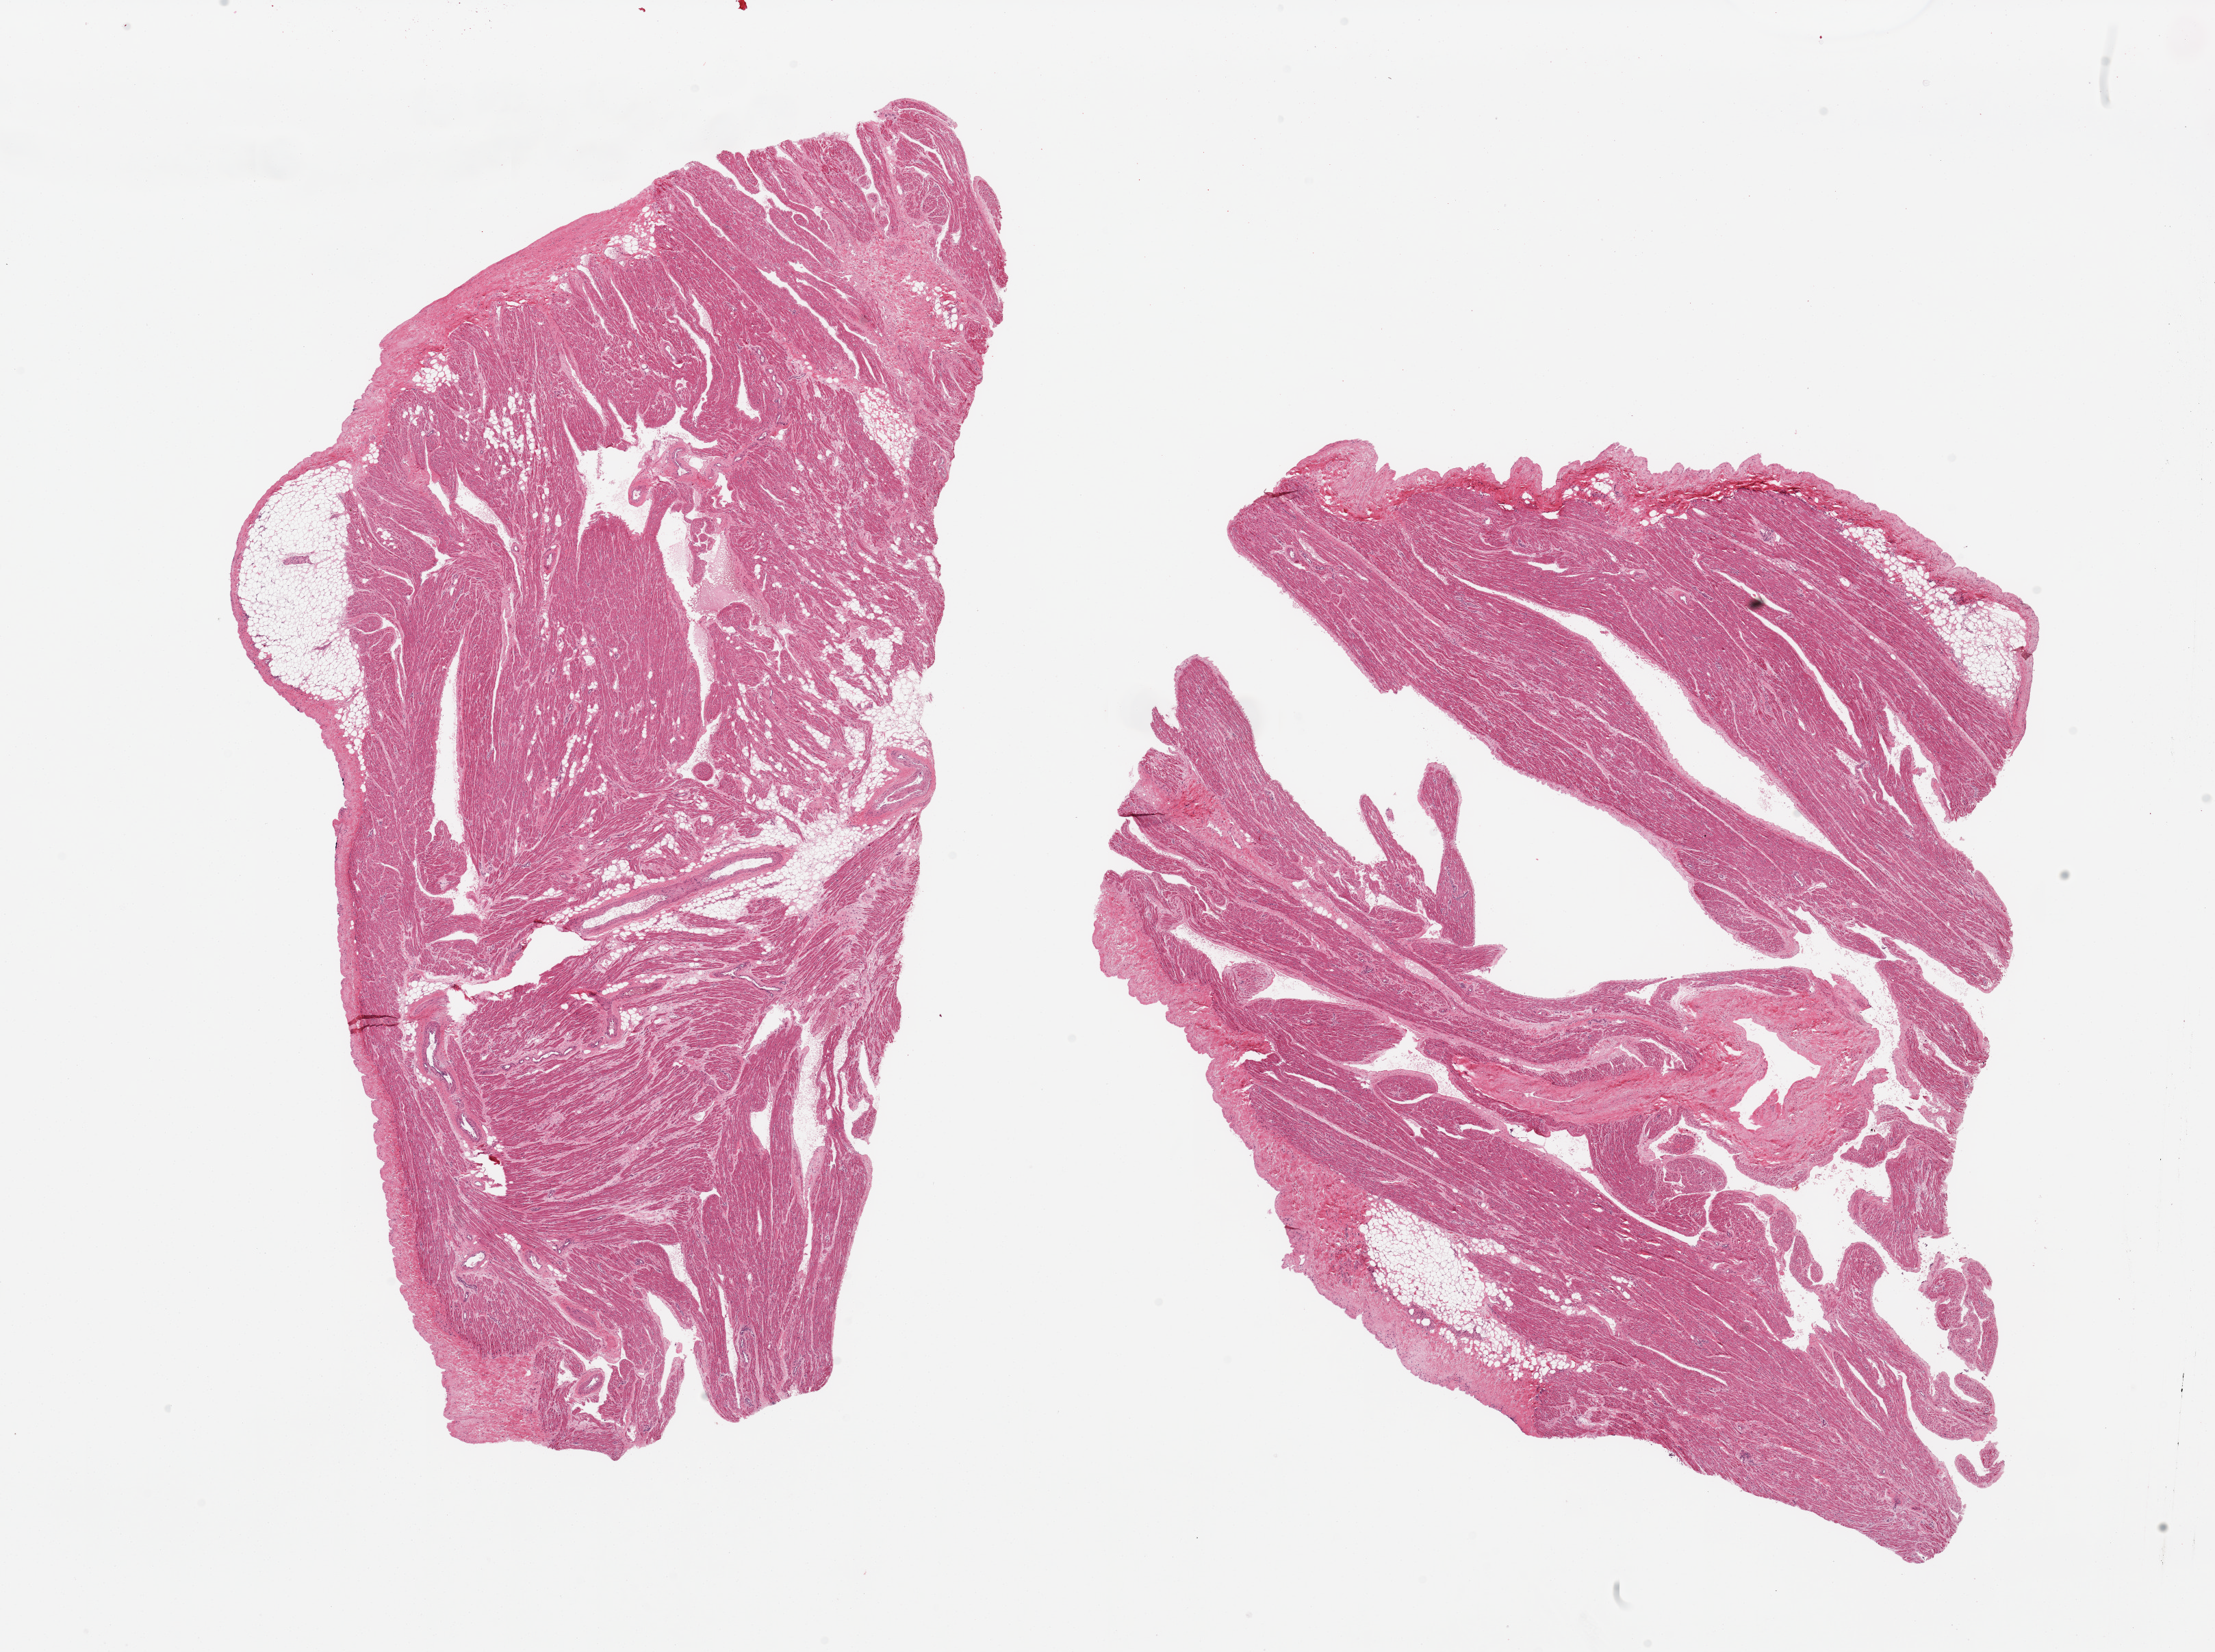
Digitized haematoxylin and eosin-stained section, low-resolution overview of the scanned area, about 25.6 x 19.1 mm; PAXgene-fixed, paraffin-embedded tissue; target tissue: auricular appendage; donor tissue sample. Male donor.
Review note (as recorded): 2 pieces; ~10% internal fat.